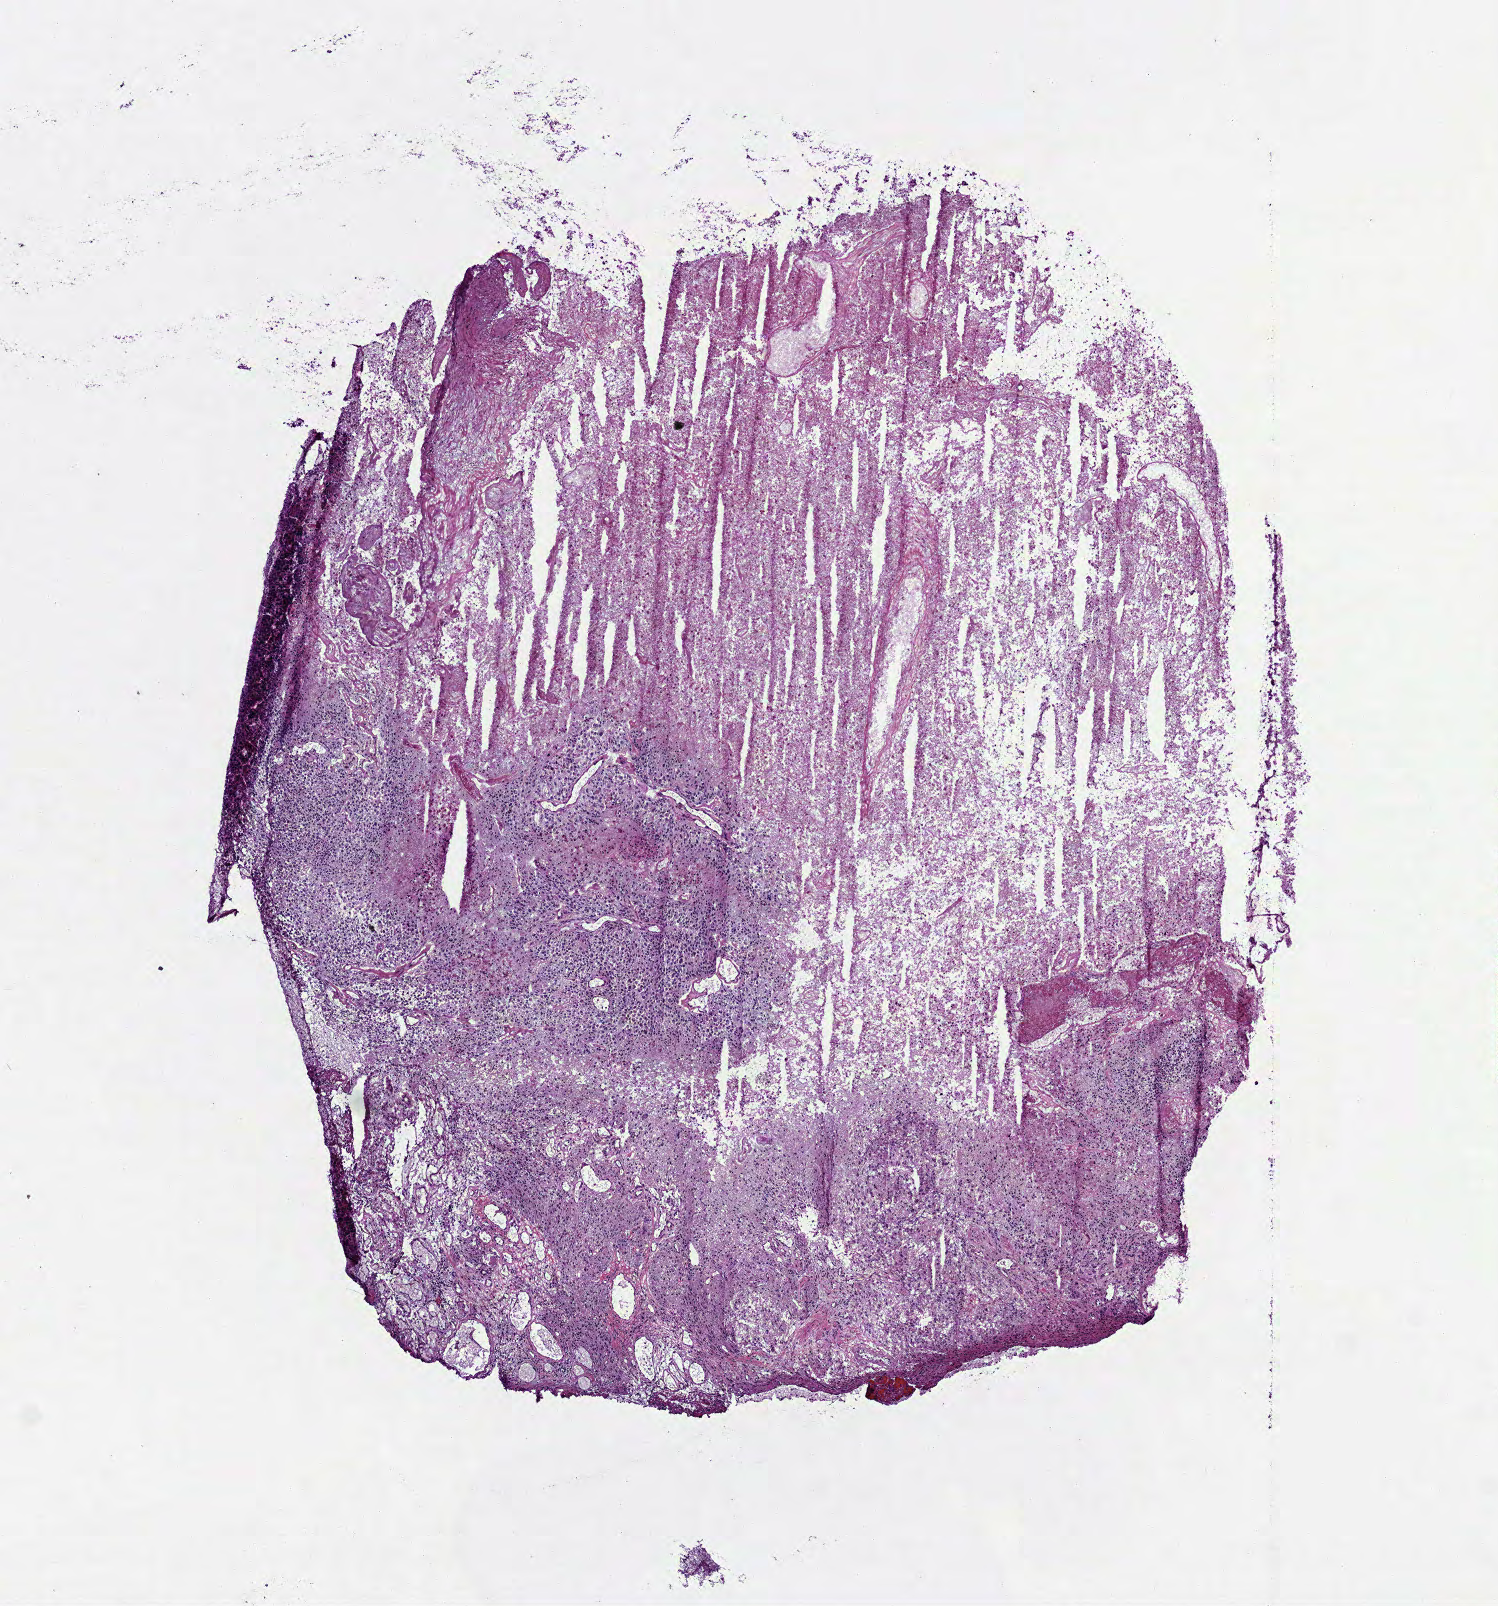
Whole-slide histology image, H&E — whole scanned area (about 6.0 x 6.5 mm) shown as a low-resolution overview; frozen section; sample: primary tumour, brain. Male, age 64 years at initial diagnosis. Pathologist review of this section (percent, as recorded): tumour cells 48%, tumour nuclei 80%, normal cells 0%, stromal cells 2%, necrosis 50%.
Pathologic diagnosis: Glioblastoma.